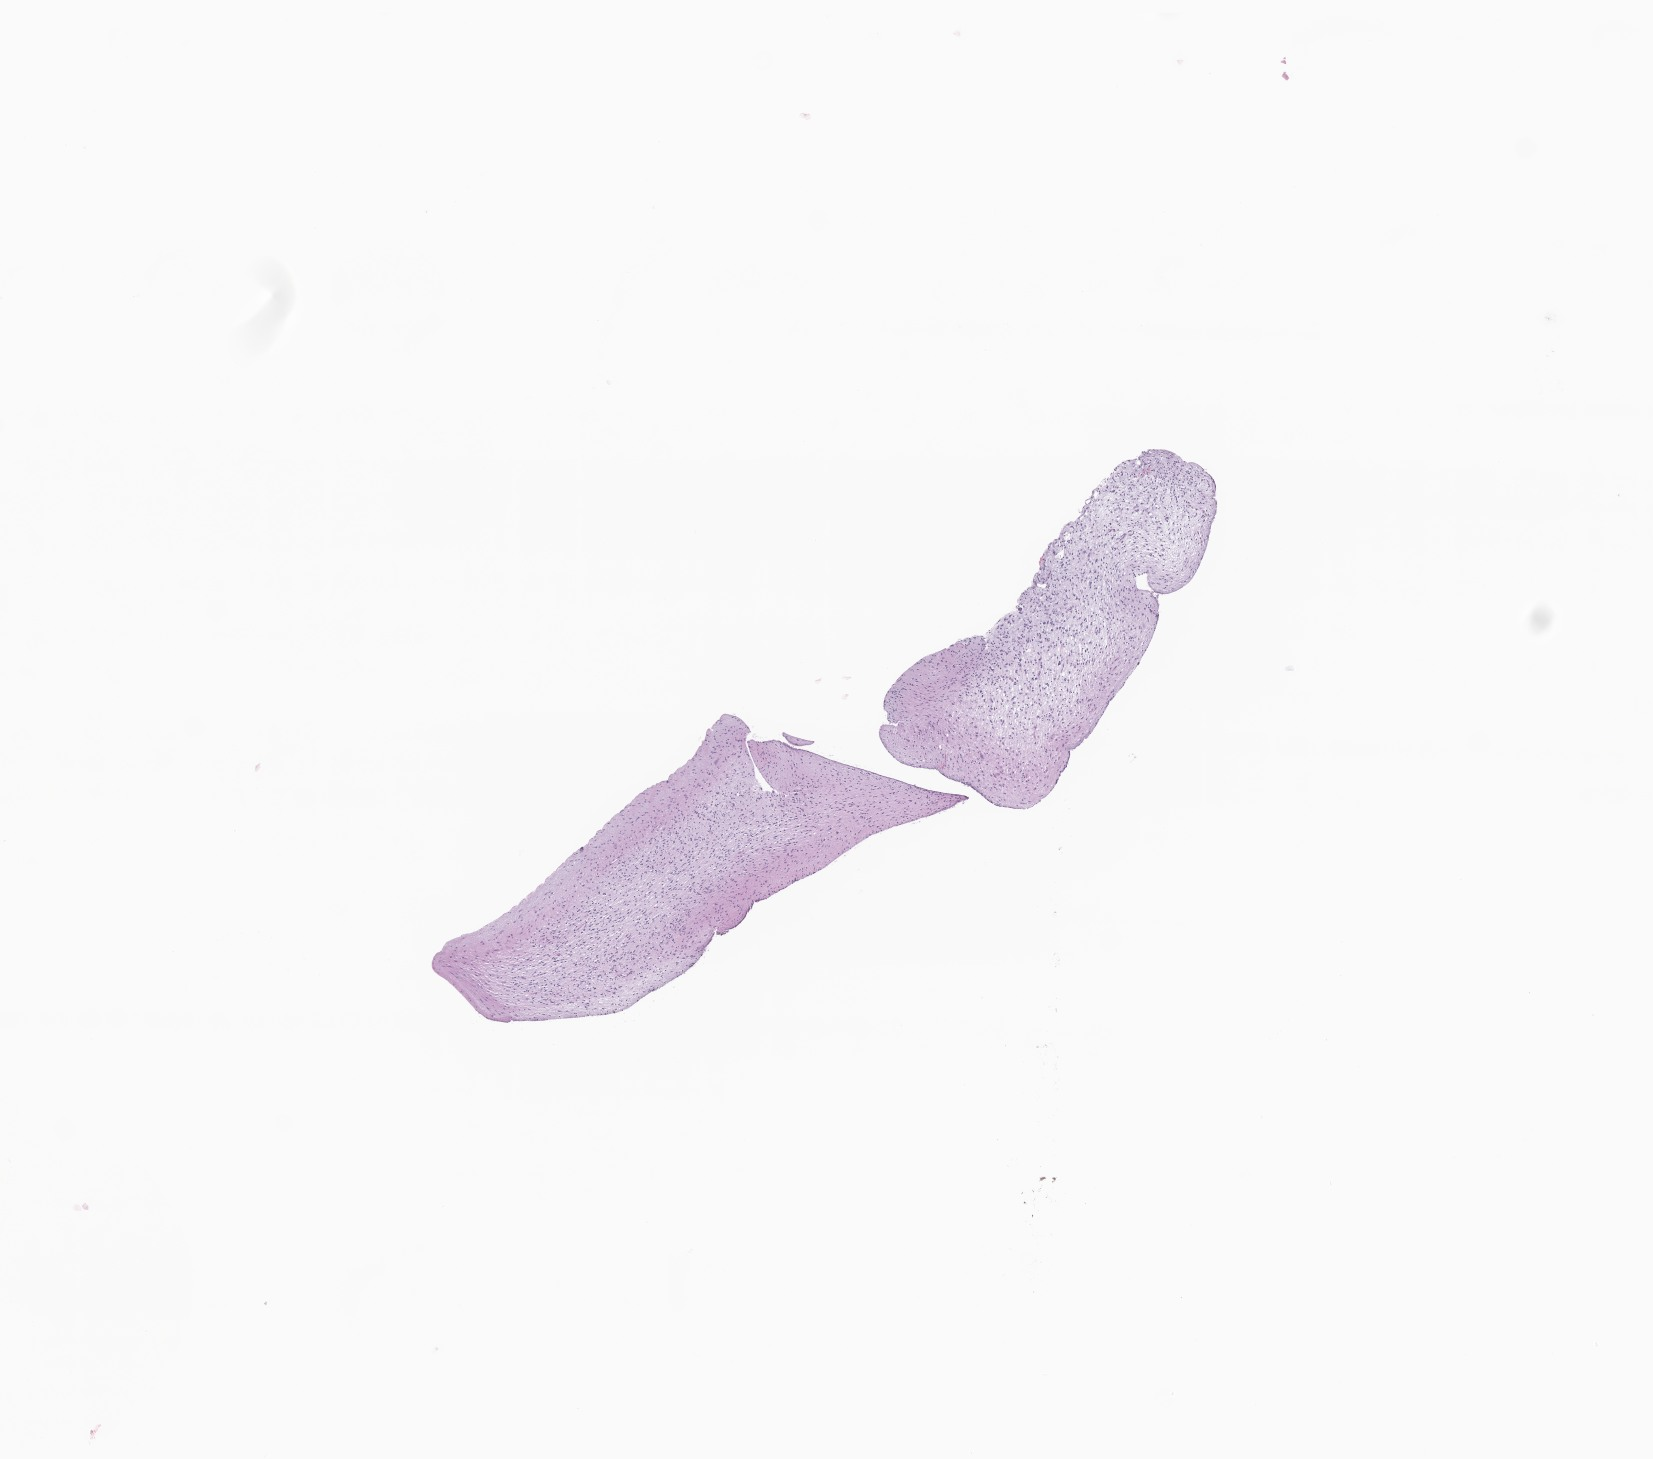
Whole-slide image, H&E stain of tumor tissue from the cerebellum — whole scanned area (about 7.0 x 6.2 mm) shown as a low-resolution overview. Formalin-fixed, paraffin-embedded (FFPE) tissue. Patient male; age 475 days (about 1.3 years).
- diagnosis (ICD-O-3 morphology term): Pilocytic astrocytoma